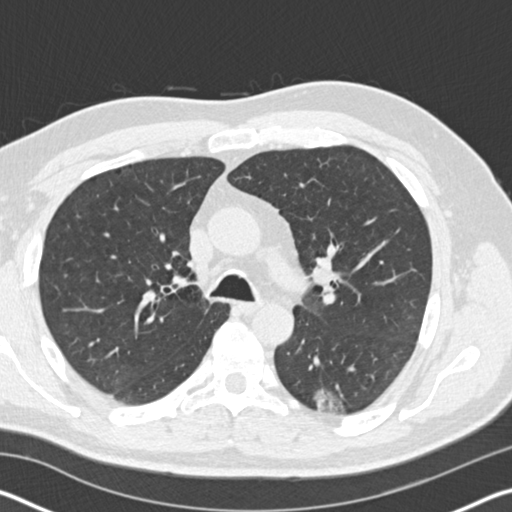
Low-dose screening chest CT, axial slice, baseline annual screen, lung window (W 1500 / L -600 HU), standard (soft-tissue) reconstruction kernel (B30f), slice 65 of 178 in the series, 512 × 512 image matrix, field of view 340 × 340 mm. Male, age 60 years at enrolment. Current smoker at enrolment.
Expert reader's lesion annotation, bounding box [x1, y1, x2, y2] px = [277, 360, 359, 425]. The screening reader recorded 3 non-calcified nodules or masses ≥4 mm on this exam (left lower lobe, right lower lobe, right lower lobe); which of them this box marks is not recorded. Later outcome: lung cancer diagnosed 171 days after this screen — papillary adenocarcinoma, NOS, left lower lobe, moderately differentiated (G2), stage IB (AJCC 6th edition), 35 mm at pathology.